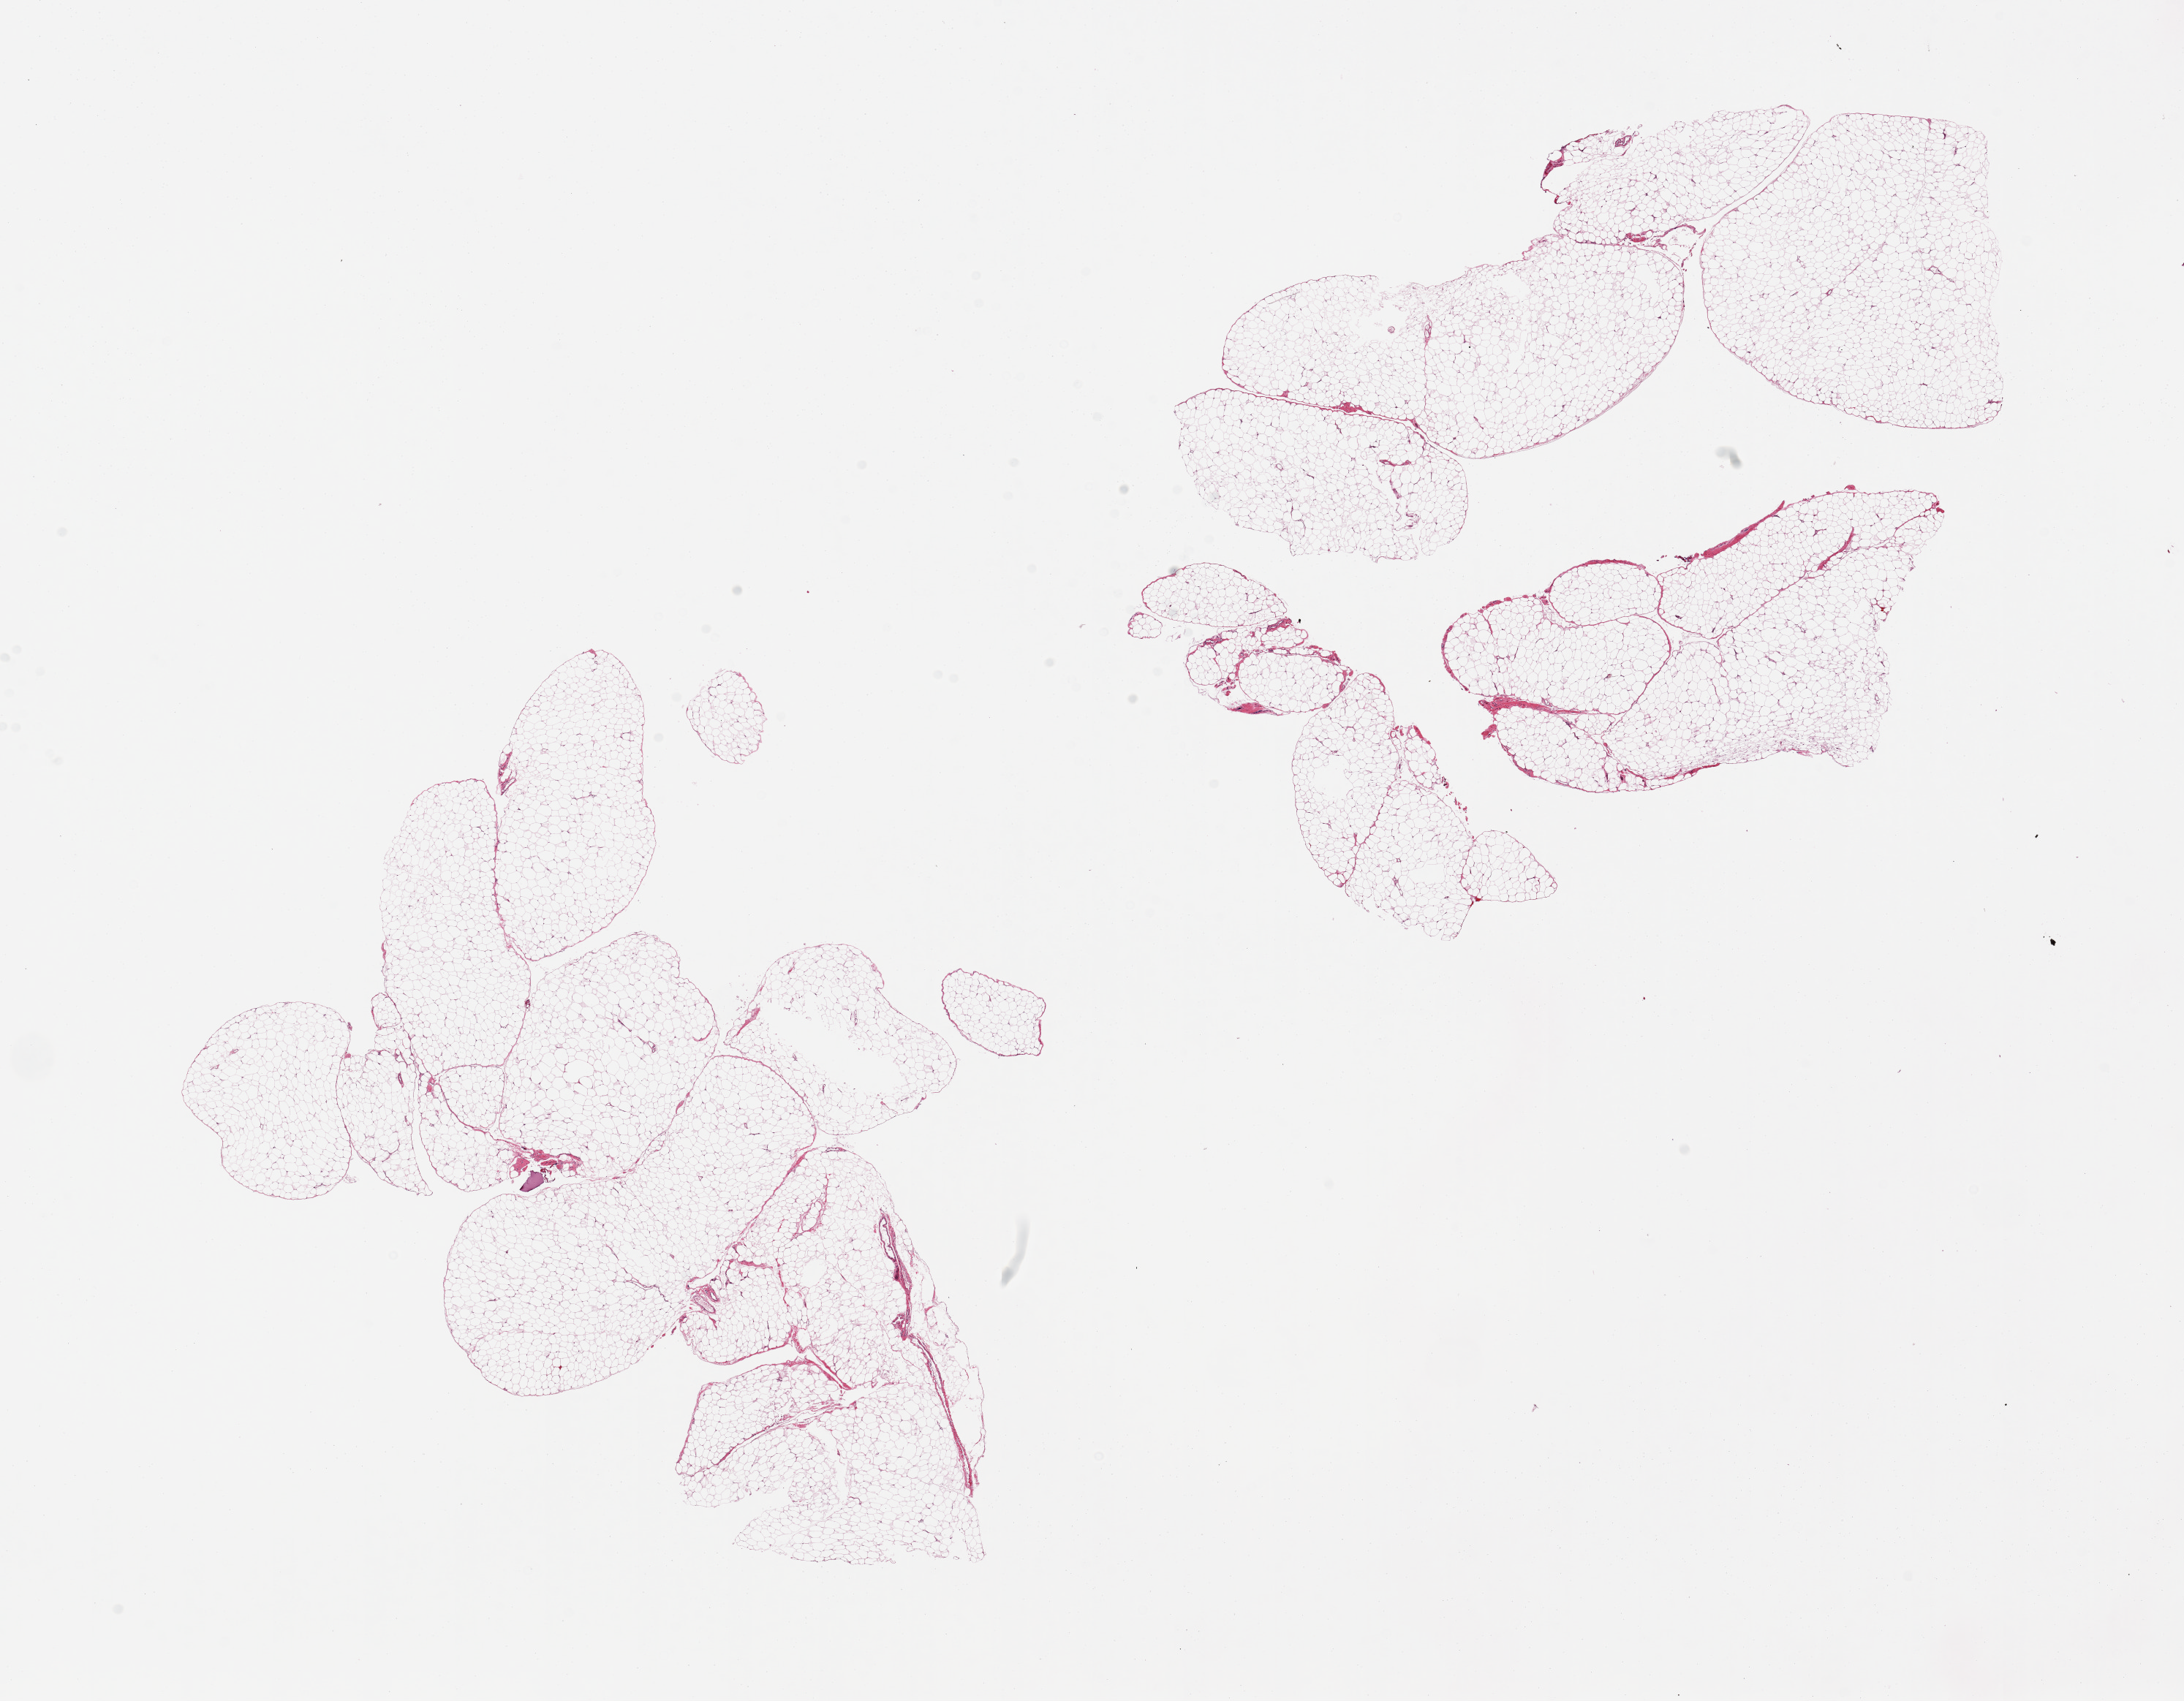
Hematoxylin and eosin (H&E) whole-slide image, shown as a low-resolution overview of the whole scanned area (about 23.6 x 18.4 mm, acquisition: 20x scan); PAXgene-fixed, paraffin-embedded tissue; sampled site (target tissue): omentum; tissue donor sample.
Reviewer comment on this tissue sample: 2 pieces, 11x8 & 11x8mm; no holes.